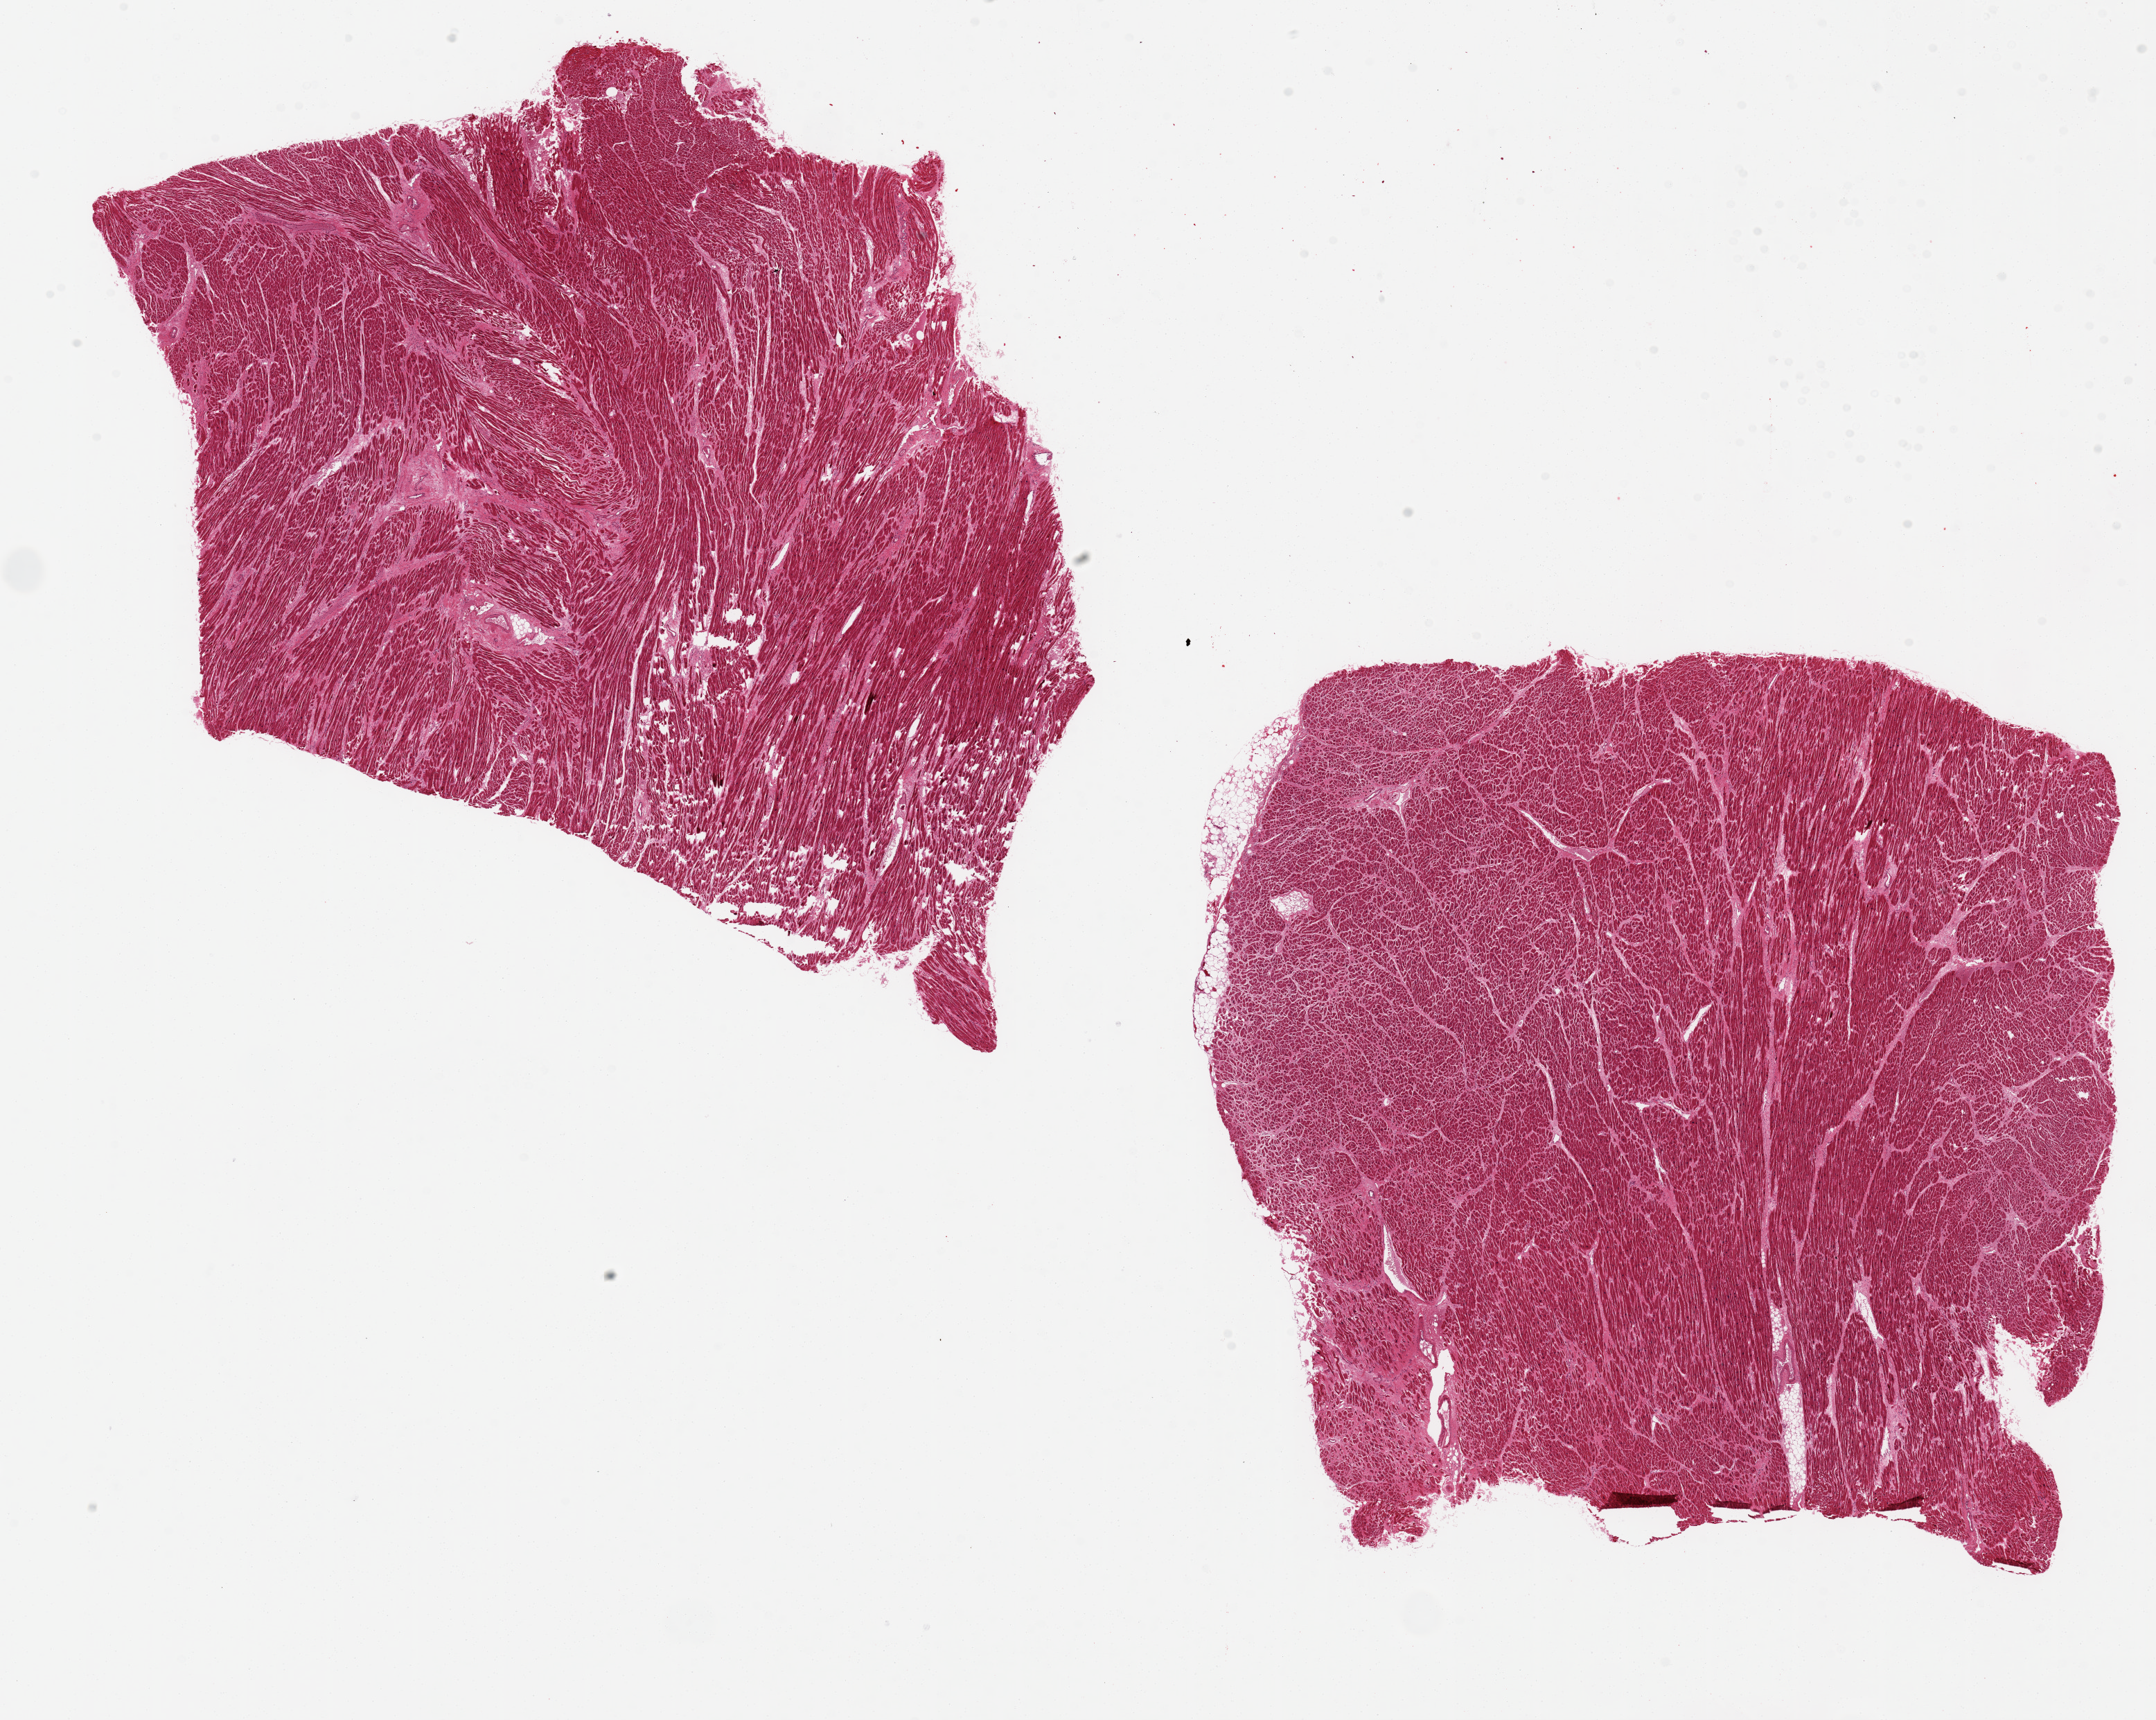
Whole-slide image, hematoxylin and eosin (H&E) stain — shown as a low-resolution overview of the whole scanned area (about 24.6 x 19.6 mm); PAXgene-fixed paraffin-embedded (PFPE) section; sampled site (target tissue): heart; donor tissue sample. Female donor.
Review note (as recorded): 2 ~ 9x8.5mm aliquots. Patchy interstital fibrosis, remote ischemic changes.